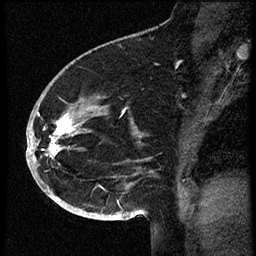
Breast MRI (dynamic contrast-enhanced), one sagittal slice. Position 38 of 60 along the scan axis. Dynamic contrast-enhanced study with each time point stored as its own series, time point 2 of 3 at this slice position (early post-contrast, ordered by acquisition time). 1.5 T. TE 4.2 ms, TR 18.9 ms. 2 mm slice thickness. 256 × 256 image matrix, field of view 200 × 200 mm. Female patient. From the clinical record (not read from this slice): setting: breast cancer imaged before/during neoadjuvant chemotherapy; receptor status: HR-positive, HER2-negative.
Outlined on this slice (semi-automatically segmented with operator editing):
- analysis volume of interest (the breast-tissue region the enhancement analysis was run in; not a lesion): bounding box [x1, y1, x2, y2] px = [30, 87, 109, 173]
- tumour enhancement mask (voxels above the 100 % enhancement threshold inside the analysis volume of interest): [30, 117, 76, 159]